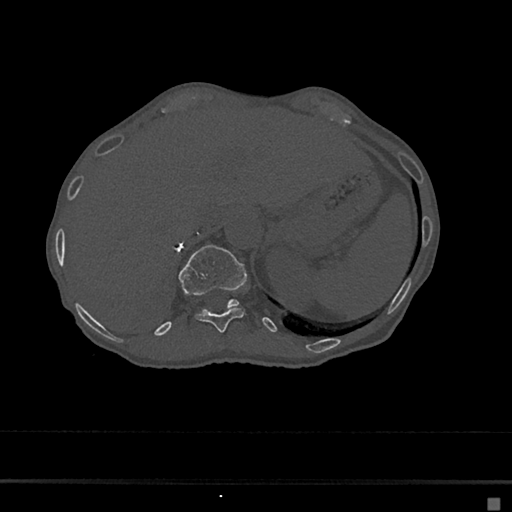
CT including the spine, one axial slice; position 157 of 797 along the scan axis; reconstruction kernel Br40s/3; bone window (W 1800 / L 400 HU); 512 × 512 image matrix. Female patient, age 68 years. From the clinical record (not read from this slice): primary cancer: renal.
Outlined on this slice (semi-automatic segmentation, software-assisted and operator-edited):
- T11 vertebra: box from (x=196, y=308) to (x=244, y=332) px
- T12 vertebra: (x=178, y=245)–(x=247, y=308)